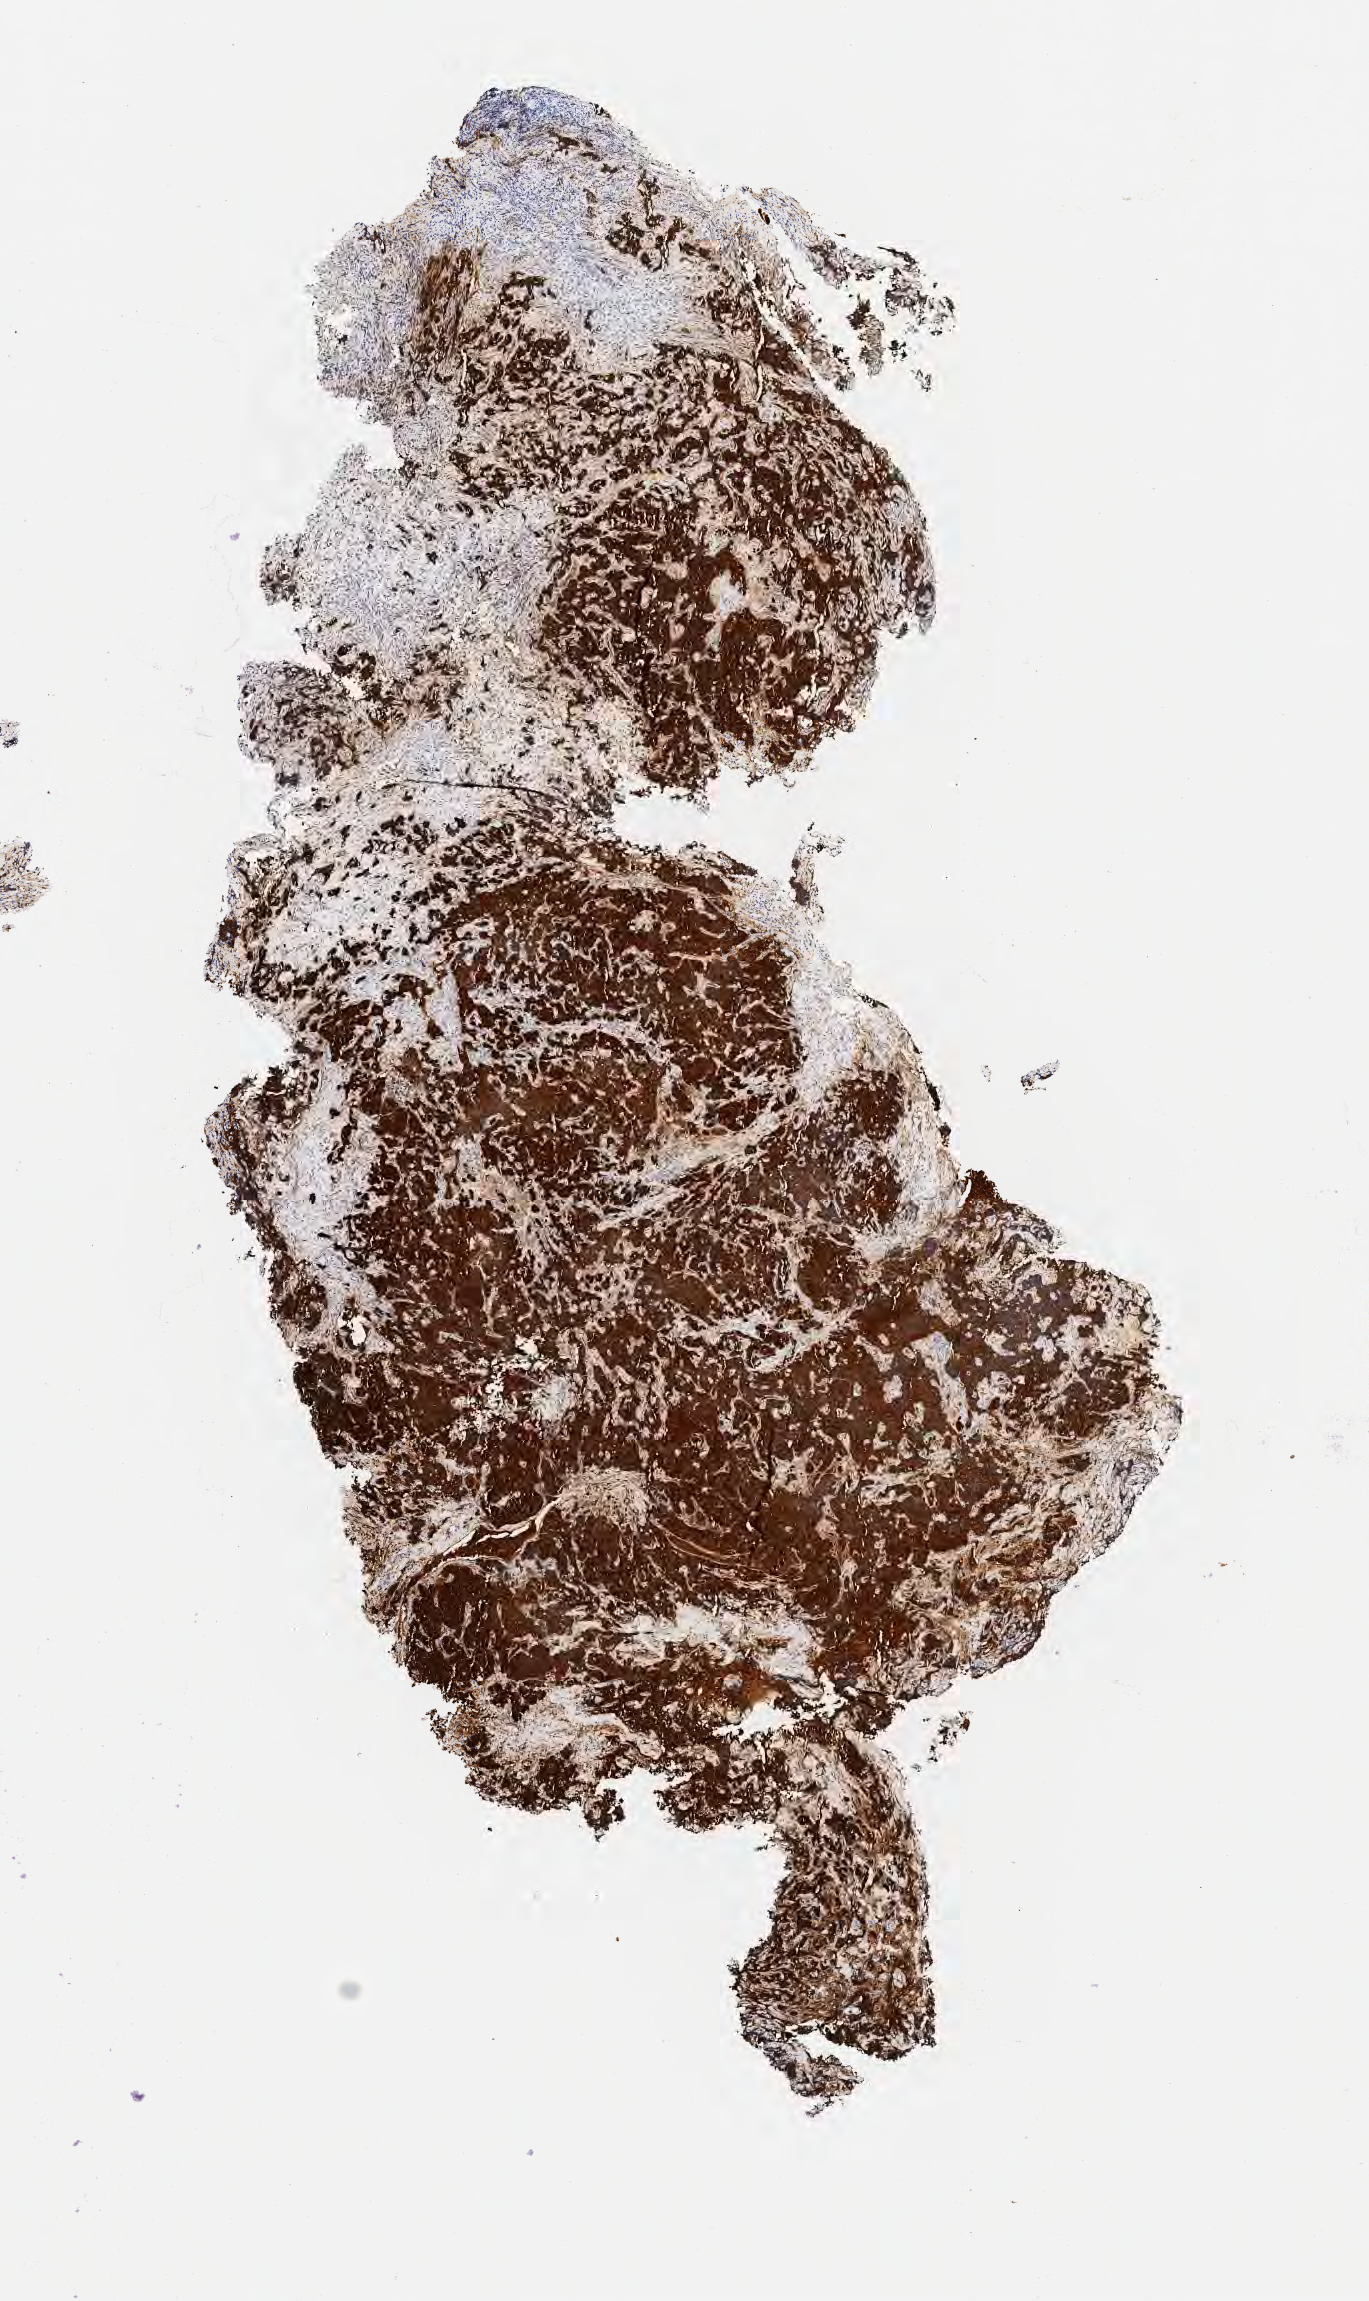
Immunohistochemistry (IHC) whole-slide image stained for p16 (p16INK4a), low-resolution overview of the scanned area, about 5.5 x 9.3 mm. Specimen: tumor tissue. Site: cervix. Female patient, 43 years old.
Histologic diagnosis: Lymphoepithelial carcinoma.